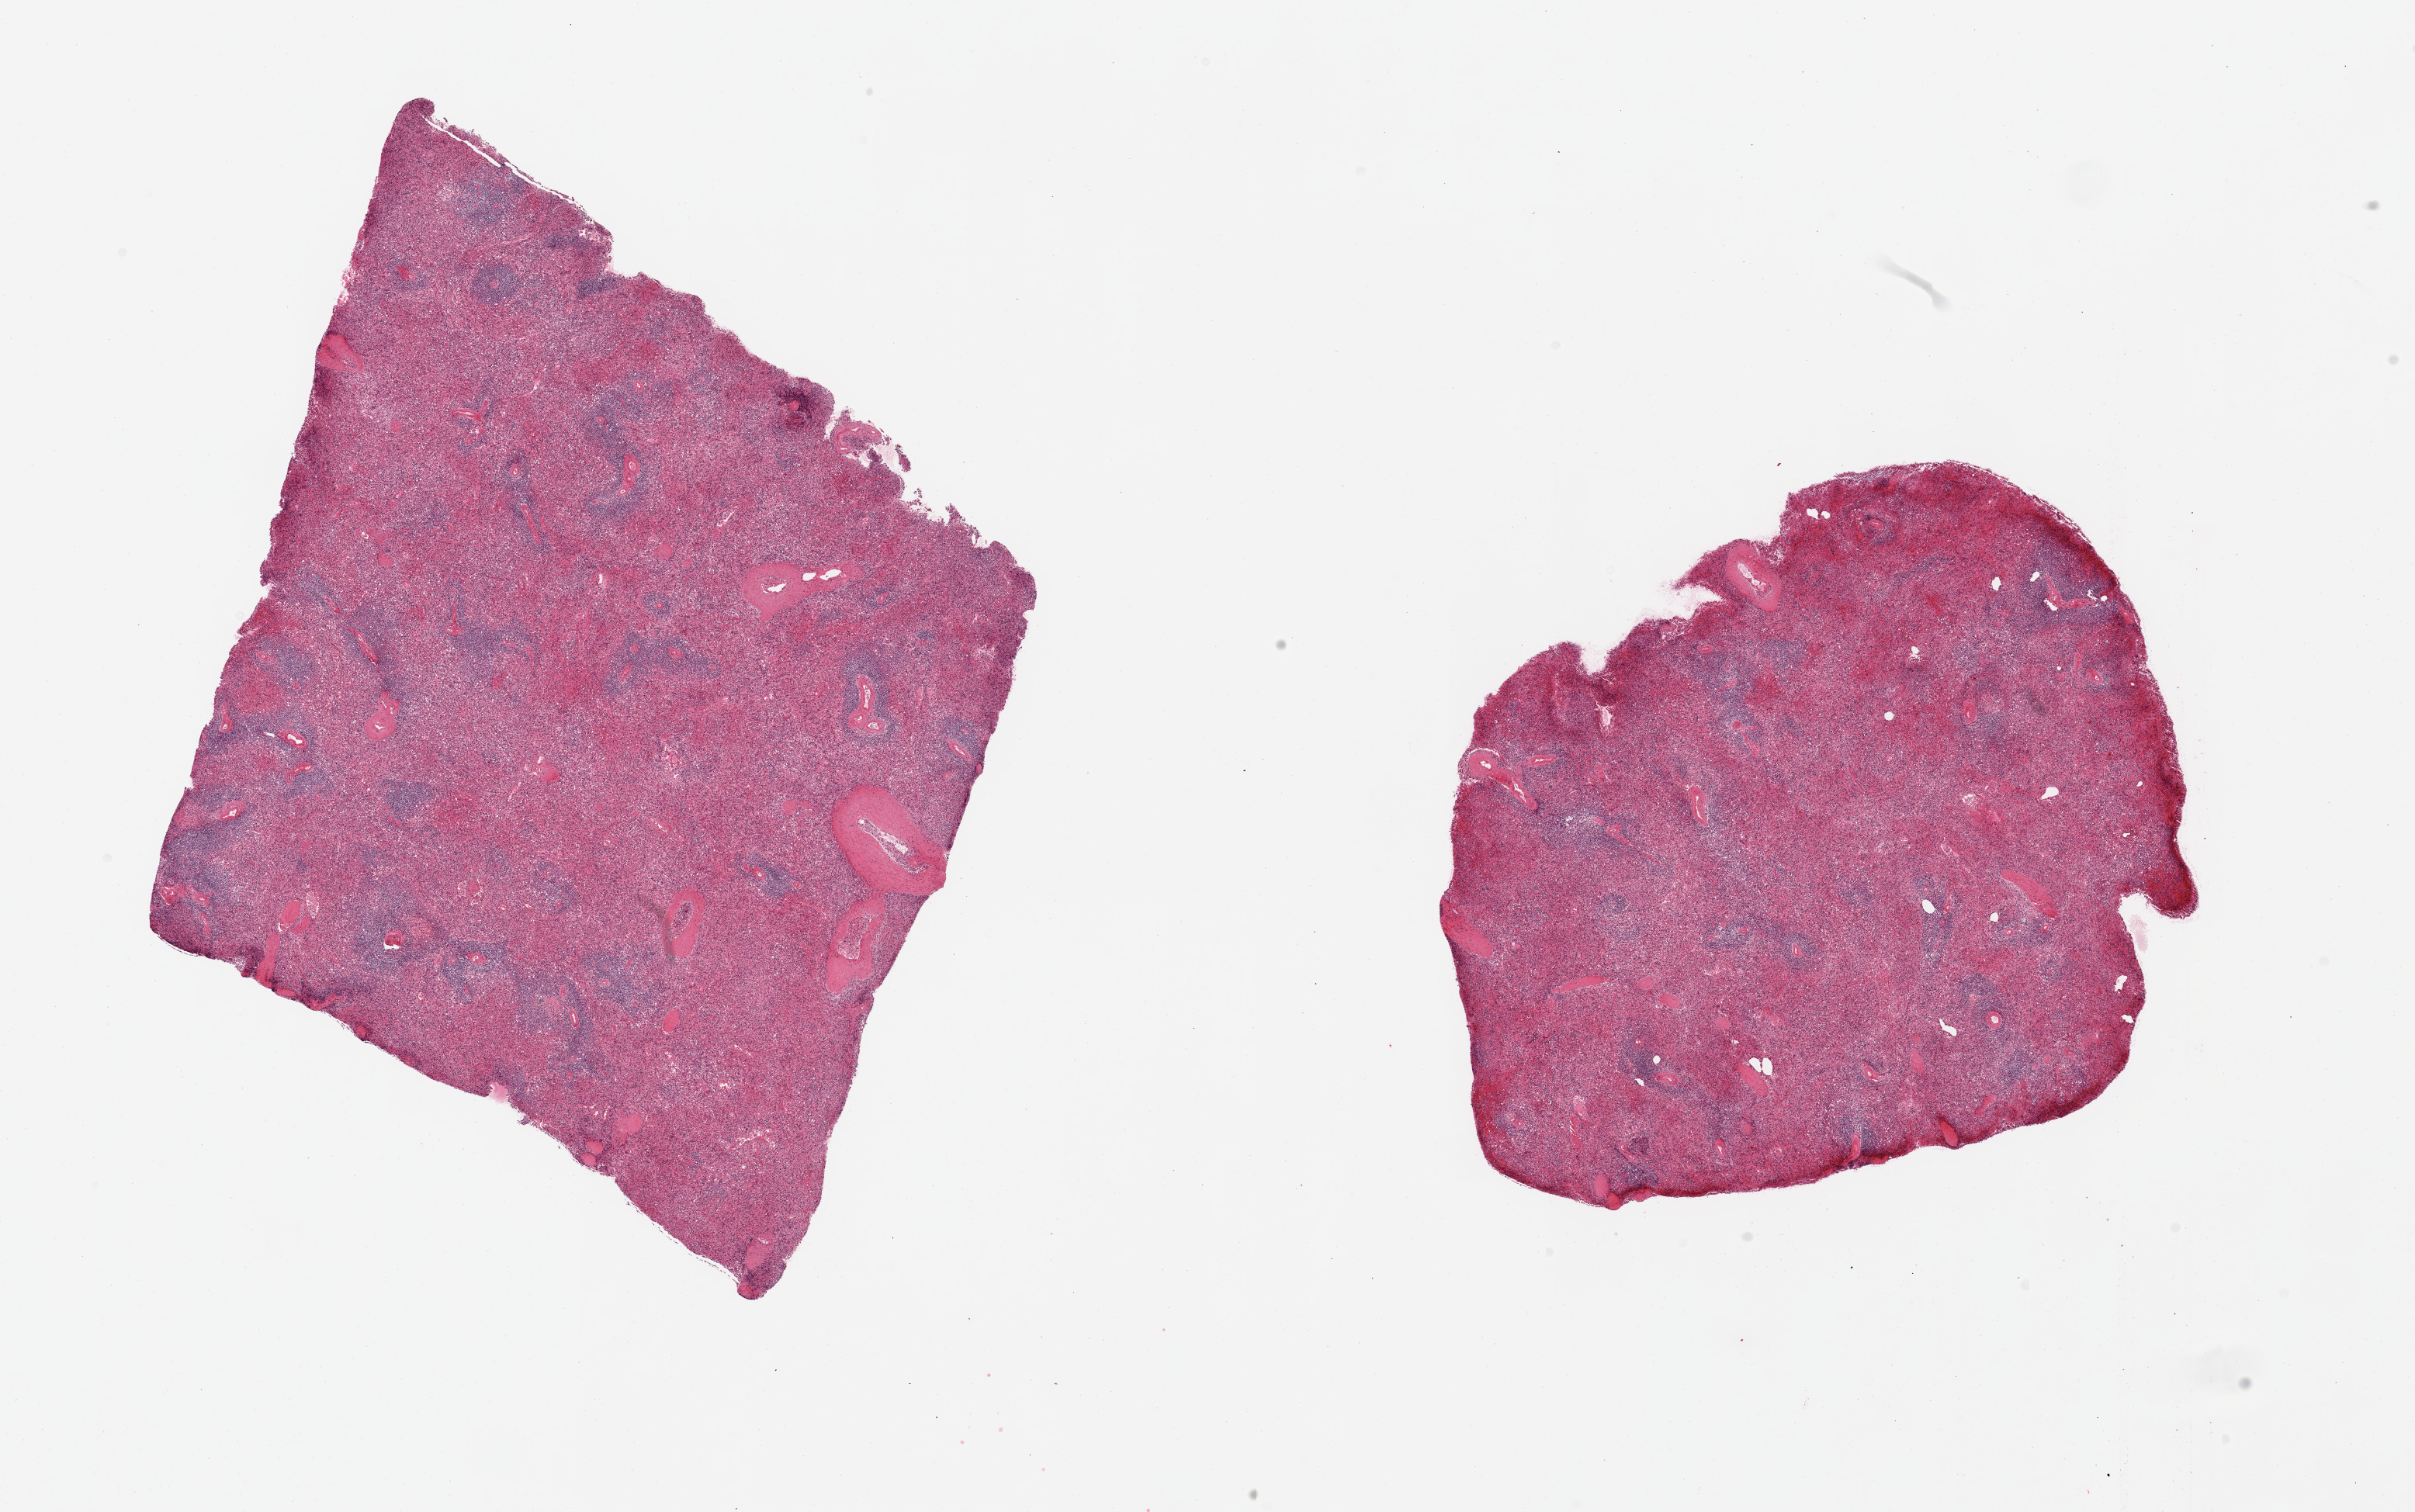
Digitized H&E-stained section, brightfield, whole scanned area (about 24.6 x 15.4 mm) shown as a low-resolution overview; PAXgene-fixed, paraffin-embedded tissue; section of spleen (target tissue); tissue donor sample. Donor: male.
• review note (as recorded): 2 pieces, moderate congestion